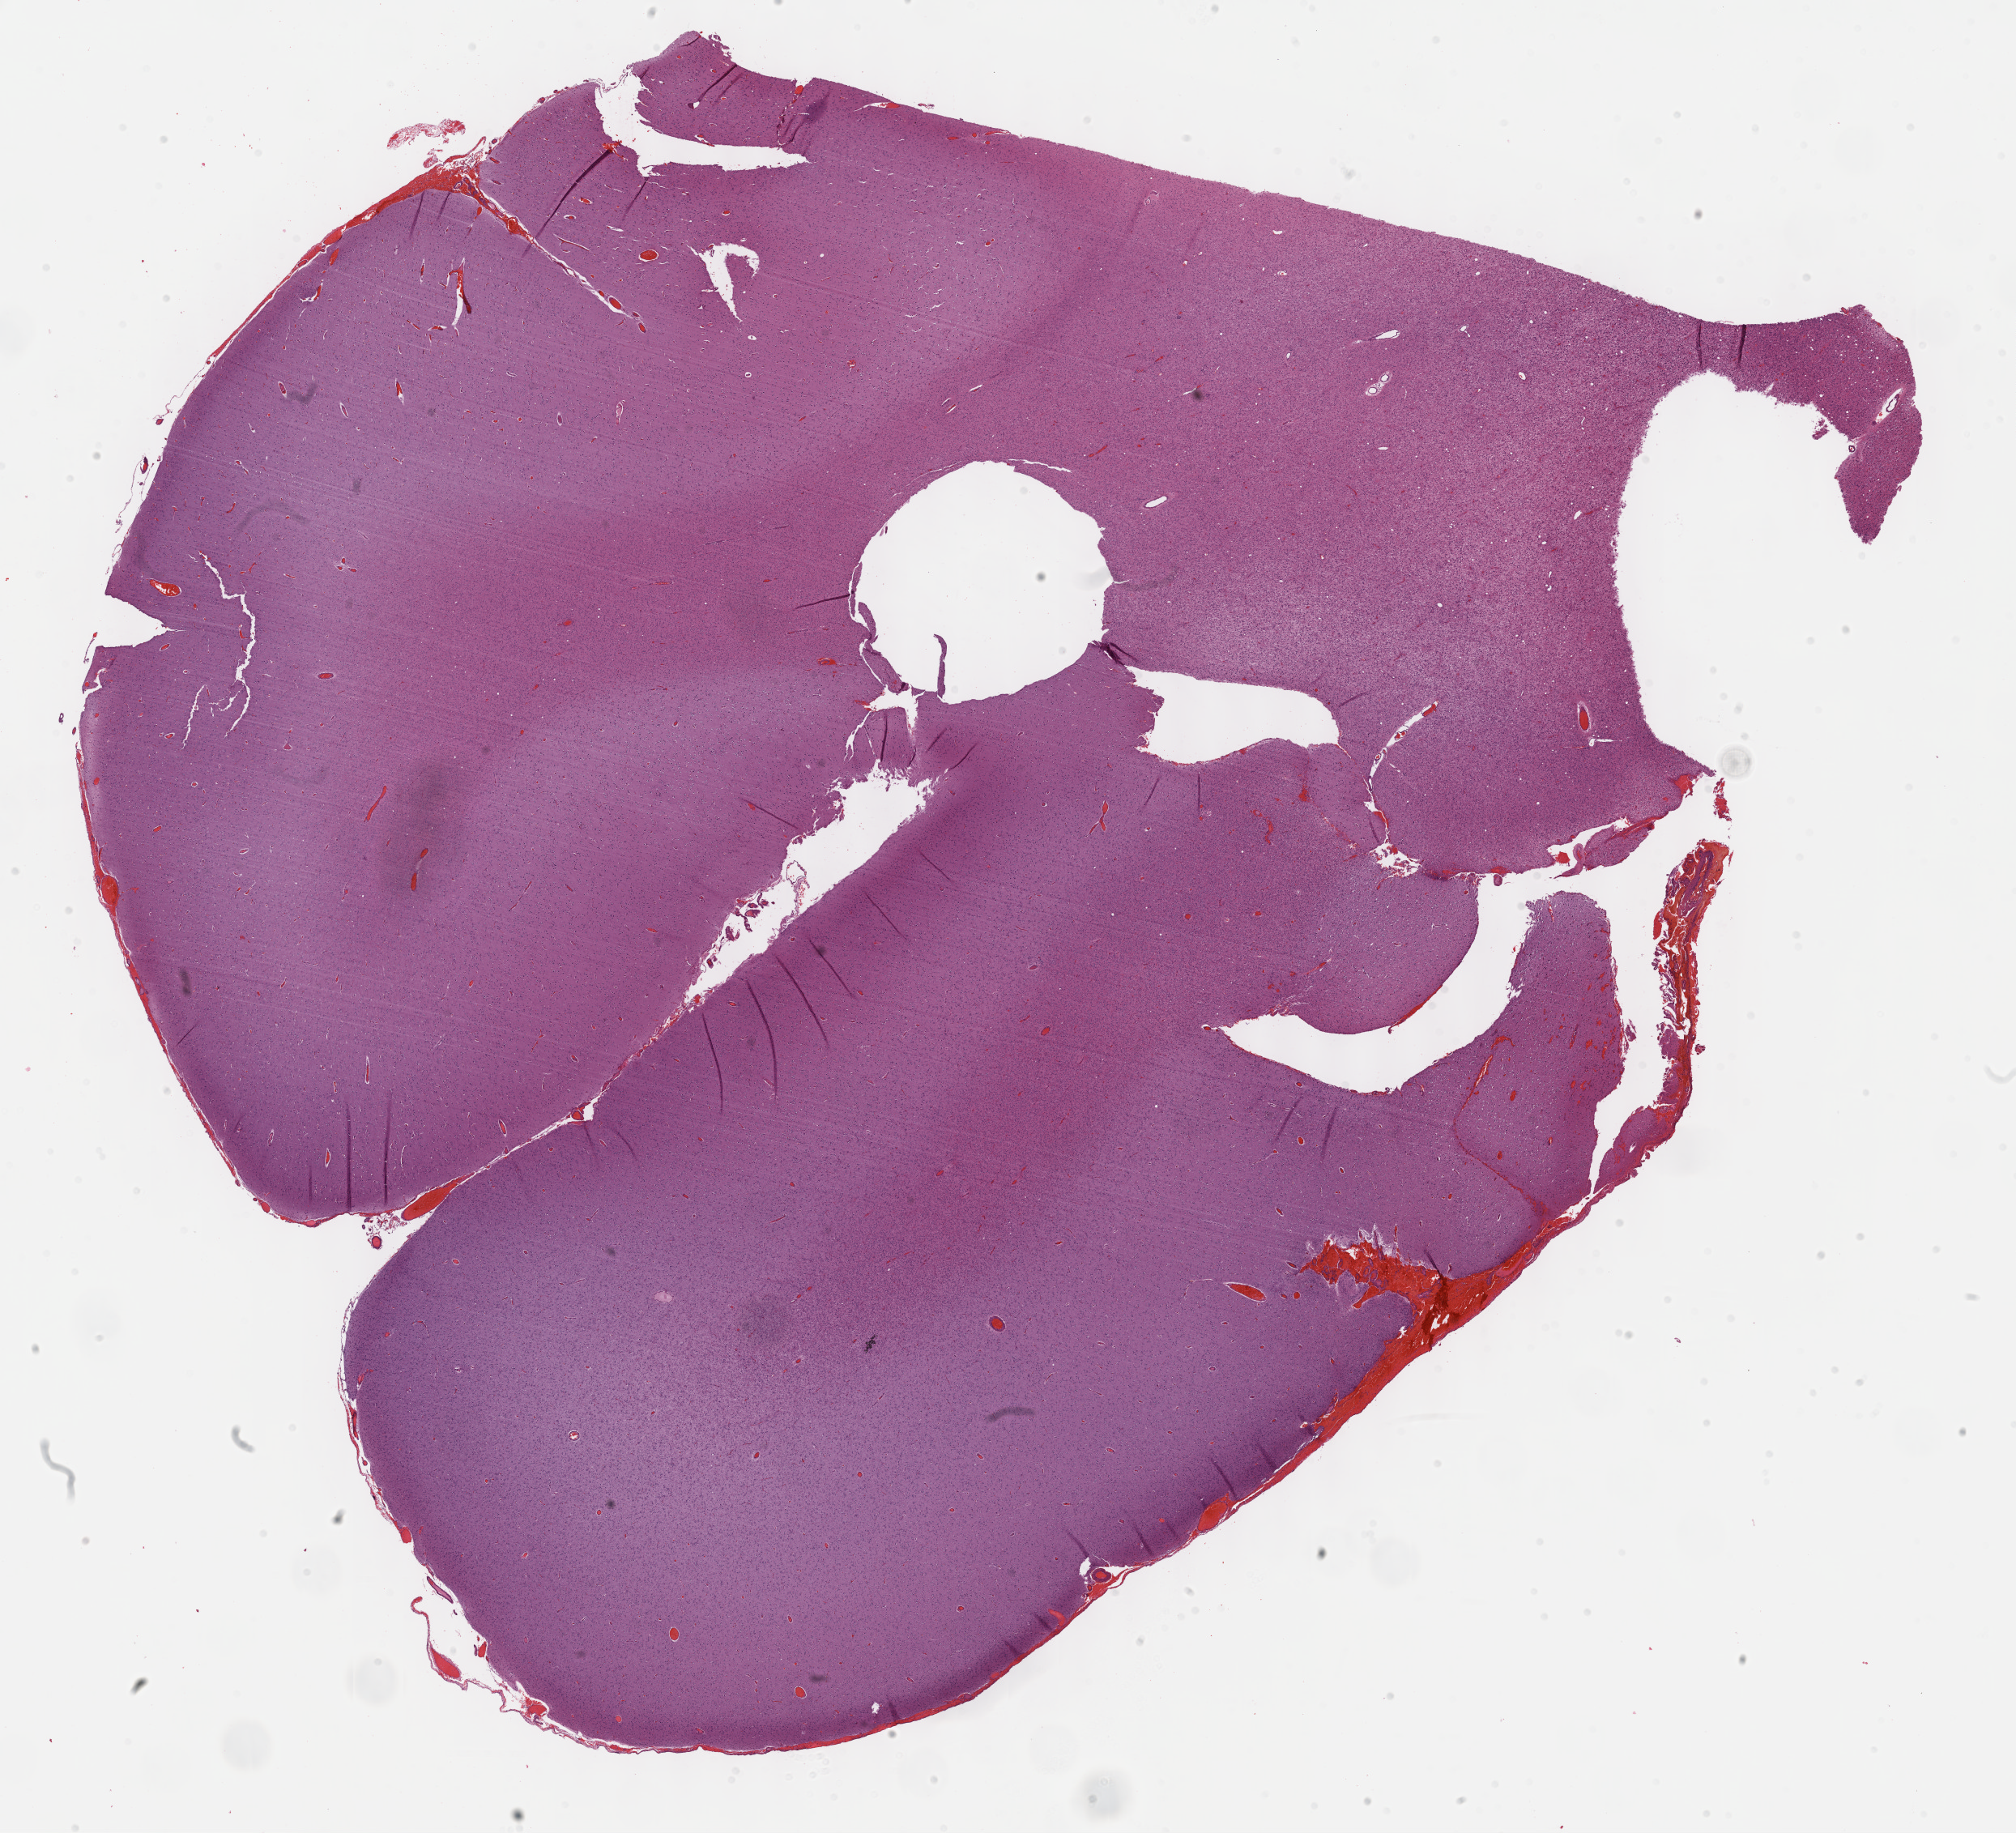
Digitized H&E tissue section (whole slide) — shown as a low-resolution overview of the whole scanned area (about 20.1 x 18.3 mm, acquisition: 40x scan), formalin-fixed paraffin-embedded (FFPE) diagnostic section, primary tumour sample from the brain. Male patient; age at initial diagnosis 33 years. Histologic grade: G2 (moderately differentiated).
- pathologic diagnosis: Oligodendroglioma, NOS